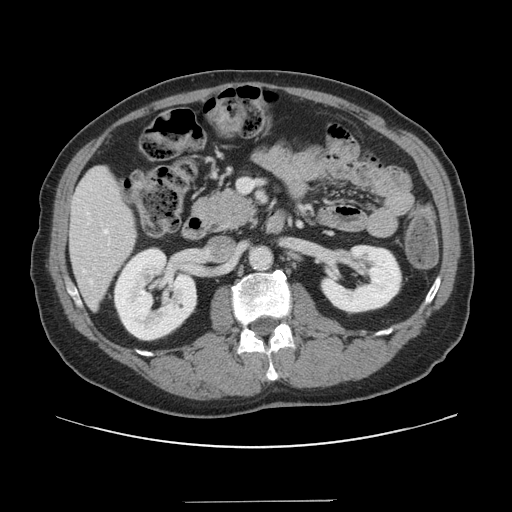
Contrast-enhanced abdominal CT, one axial slice. Position 59 of 151 along the scan axis. Intravenous contrast given. Soft-tissue window (W 400 / L 40 HU). 2.5 mm slice thickness. 512 × 512 image matrix, field of view 399 × 399 mm. Male patient, age 63 years. Case-level facts recorded for this patient, not image findings: diagnosis: colorectal cancer liver metastases, imaged before liver resection; multiple liver metastases: no; largest metastasis: 2.1 cm; chemotherapy before resection: no.
Annotated regions visible in this slice (outlined manually by an expert reader):
- hepatic veins: bounding box [x1, y1, x2, y2] px = [104, 230, 108, 234]
- liver: [71, 168, 136, 306]
- planned liver remnant (the part of the liver to remain after resection): [70, 168, 136, 306]
- portal vein (with intrahepatic branches): [238, 179, 255, 193]